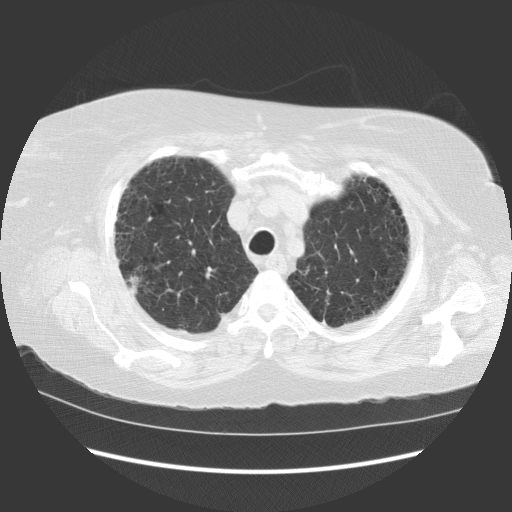
Axial slice from a low-dose chest CT screening exam; baseline screening round; lung window (W 1500 / L -600 HU); 2.5 mm slice thickness; standard (soft-tissue) reconstruction kernel (STANDARD); slice 98 of 121 in the series; 512 × 512 image matrix, field of view 380 × 380 mm. Female, age 64 years at enrolment.
Expert reader's lesion annotation, bounding box [x1, y1, x2, y2] px = [111, 263, 155, 307]. The screening reader recorded 2 non-calcified nodules or masses ≥4 mm on this exam; which of them this box marks is not recorded. Official screen result: positive, change unspecified: nodule(s) >= 4 mm or enlarging nodule(s), mass(es), or other non-specific abnormalities suspicious for lung cancer. Participant outcome: lung cancer diagnosed 69 days after this screen — small cell carcinoma, NOS, right upper lobe, stage IV (AJCC 6th edition), 20 mm at pathology.